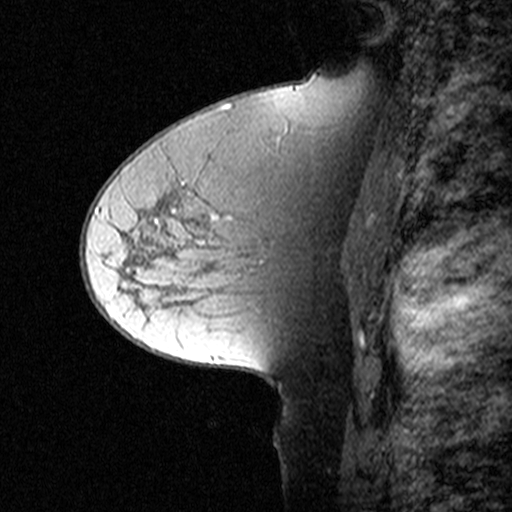
Breast MRI (dynamic contrast-enhanced), one sagittal slice; slice 29 of 44 in the series (ordered by position); dynamic contrast-enhanced study with each time point stored as its own series, time point 2 of 3 at this slice position (early post-contrast, ordered by acquisition time); 1.5 T; TE 4.5 ms, TR 11 ms; 3 mm slice thickness; 512 × 512 image matrix. Female patient, age 50 years. Case-level facts recorded for this patient, not image findings: setting: breast cancer imaged before/during neoadjuvant chemotherapy; receptor status: HR-positive, HER2-negative.
Structures marked on this image (semi-automatically segmented with operator editing):
- analysis volume of interest (the breast-tissue region the enhancement analysis was run in; not a lesion): bounding box <126,162,329,291> (left, top, right, bottom; pixels)
- tumour enhancement mask (voxels above the 90 % enhancement threshold inside the analysis volume of interest): <214,217,232,220>